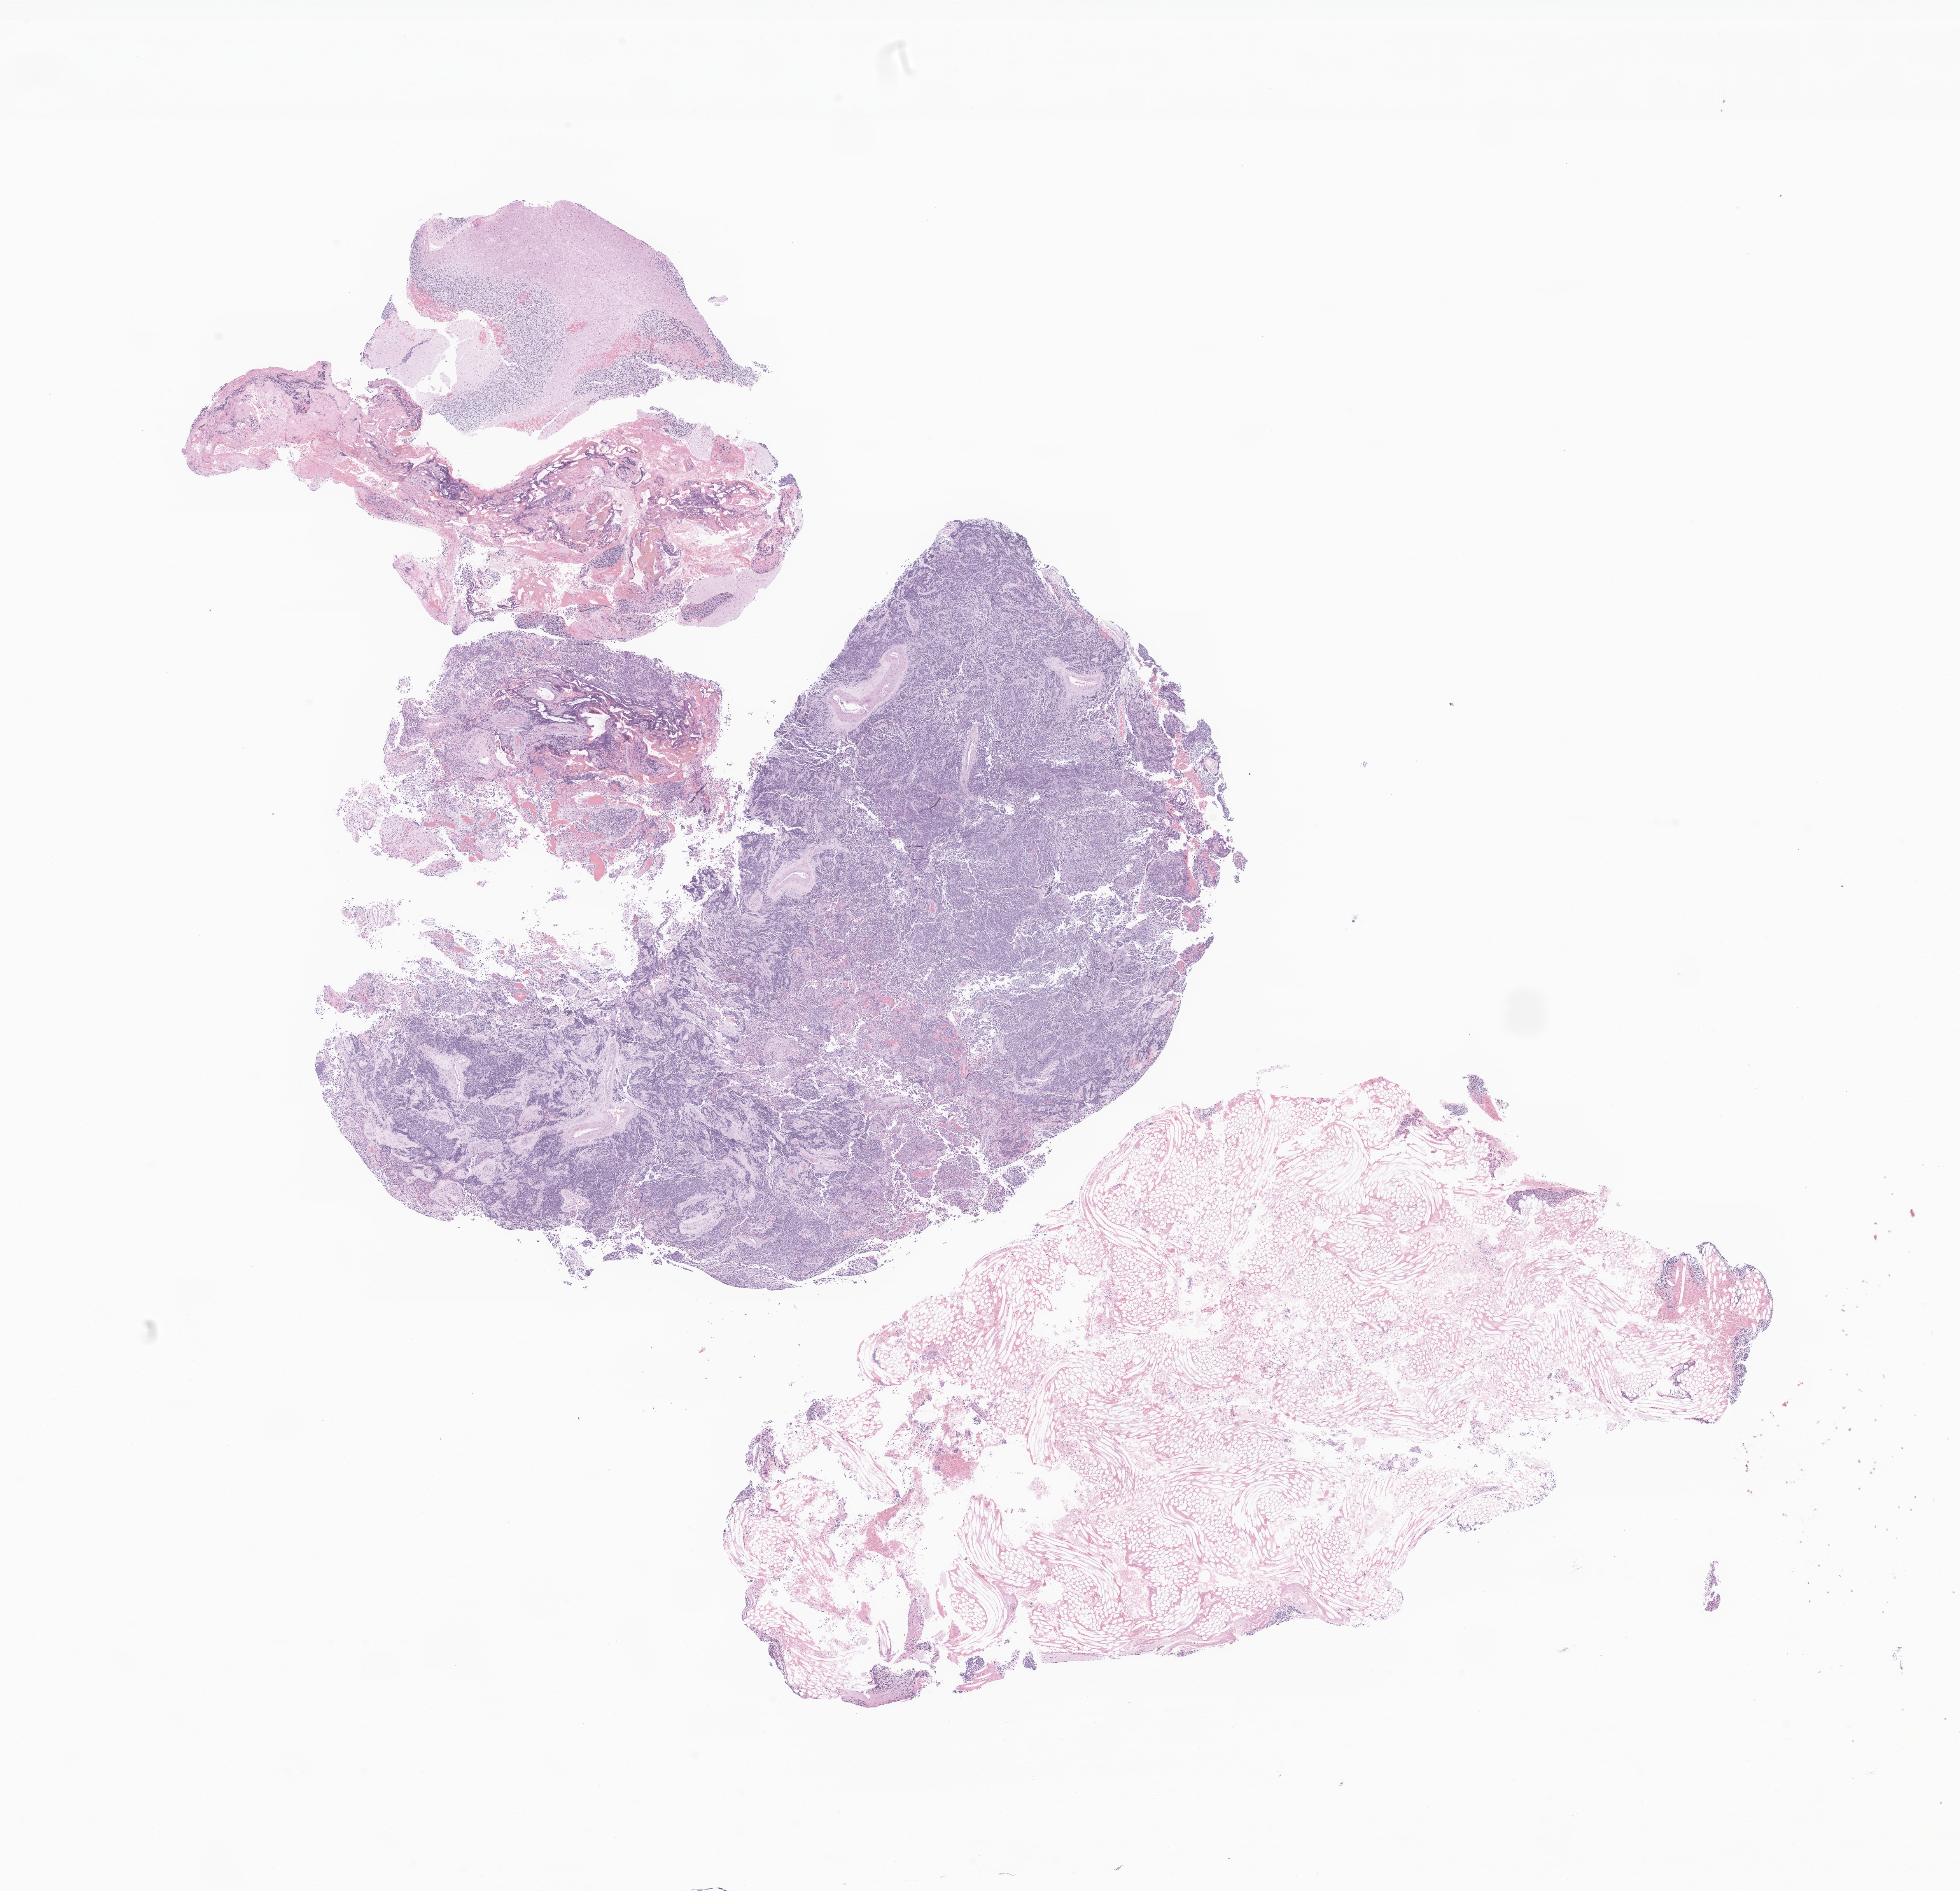
Haematoxylin and eosin whole-slide image of tumor tissue from the cerebellum, whole scanned area (about 21.2 x 20.5 mm) shown as a low-resolution overview, formalin-fixed, paraffin-embedded (FFPE) tissue. Male patient, age 40 months (3 years 4 months).
Diagnosis: Glioma, malignant.